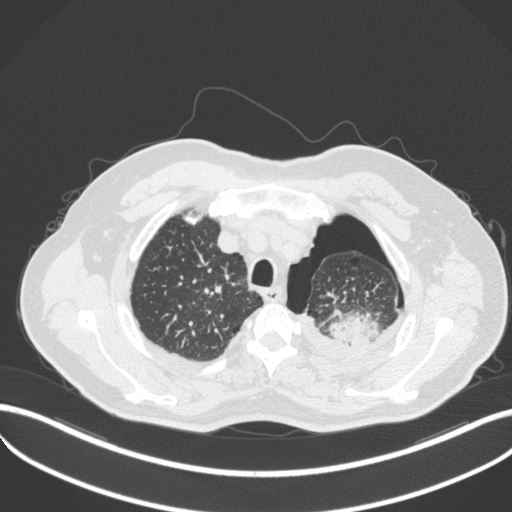
Chest CT, one axial slice; position 415 of 466 along the scan axis; reconstruction kernel B31f; 120 kVp; lung window (W 1500 / L -600 HU); 1 mm slice thickness; 512 × 512 image matrix. Patient: male, 76 years. From the clinical record (not read from this slice): clinical TNM (as recorded): T3 N0 M1b.
Outlined on this slice (rectangle marked by the reading radiologist):
- lung tumour (recorded histology: adenocarcinoma): bounding box <321,312,382,349> (left, top, right, bottom; pixels)